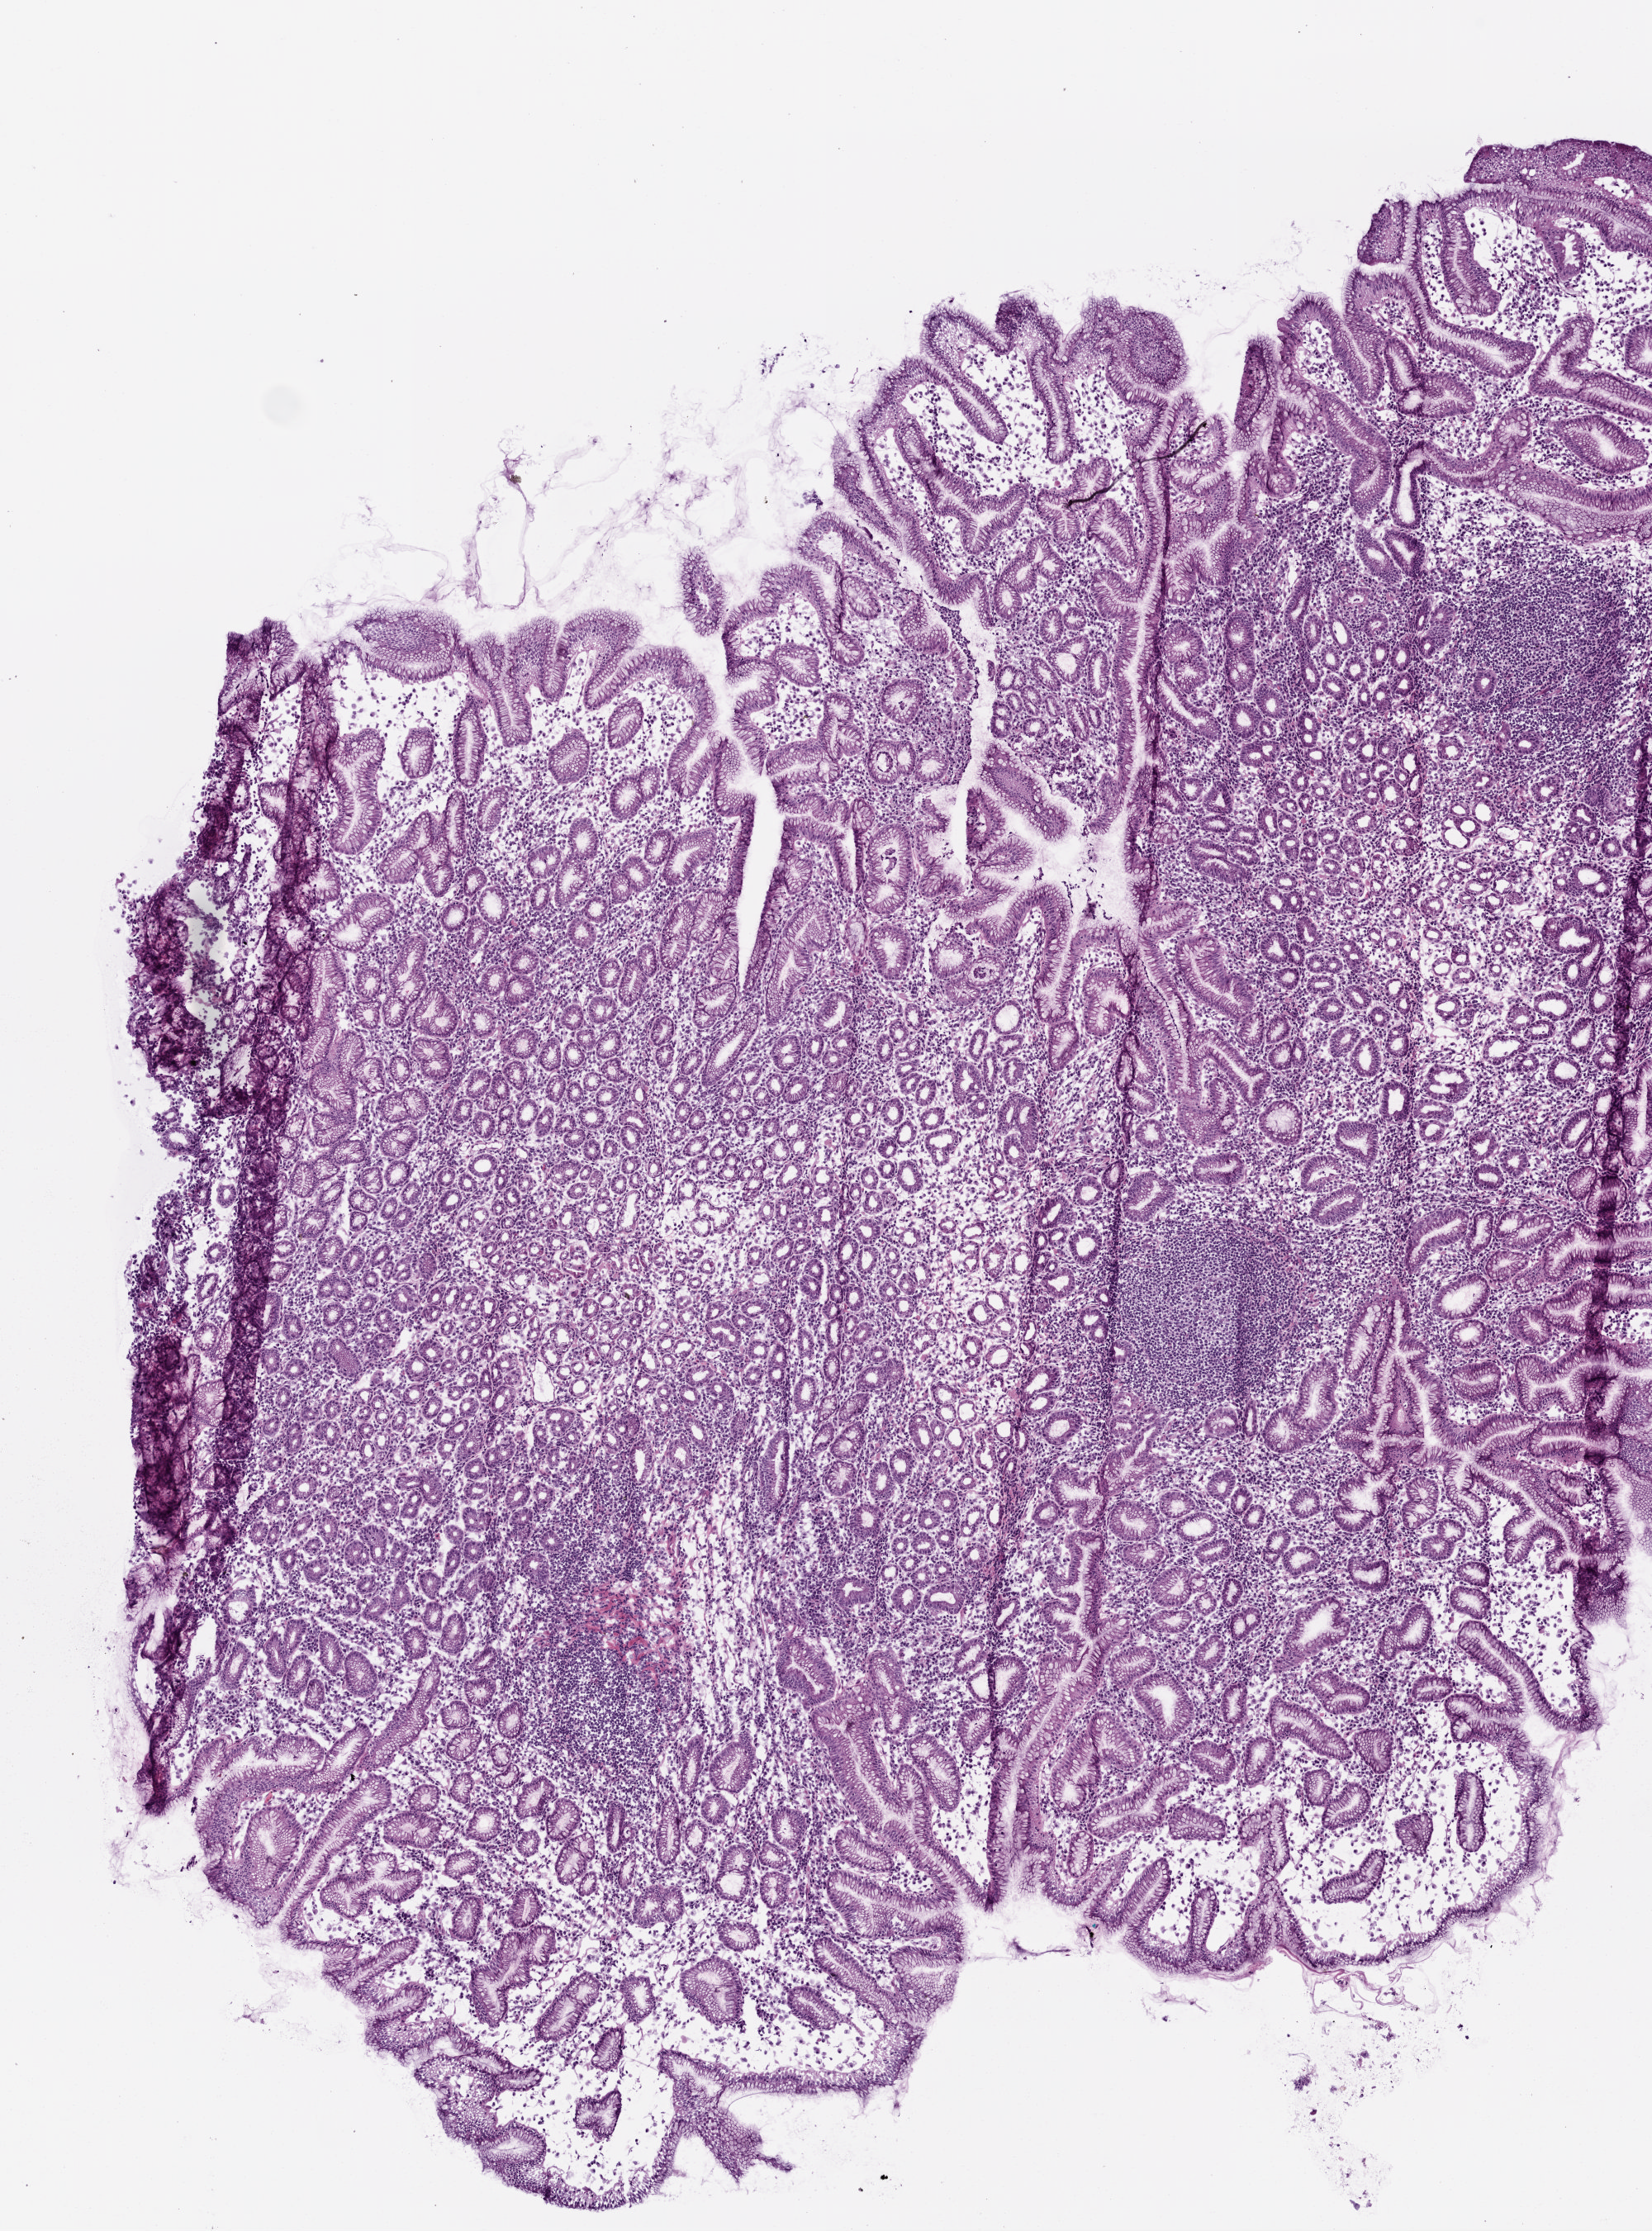
Hematoxylin and eosin (H&E) stained whole-slide image, a low-resolution overview of the entire scanned area, about 4.0 x 5.4 mm (from a 20x scan); frozen section from the top of the tissue portion; stomach, solid tissue normal (non-tumour tissue) sample. Patient: male, age at initial diagnosis 73 years.
This section: solid tissue normal sample (biorepository sample class). Patient diagnosis: Adenocarcinoma, intestinal type (gastric antrum).